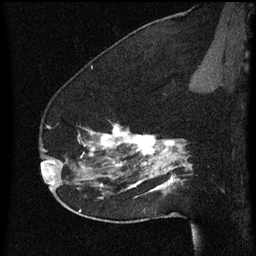
Breast MRI (dynamic contrast-enhanced), one sagittal slice. Dynamic contrast-enhanced series, image 2 of 3 at this slice position (ordered by acquisition). 1.5 T. TE 4.2 ms, TR 8 ms. 2 mm slice thickness. 256 × 256 image matrix. Female patient, age 52 years.
Outlined on this slice (semi-automatically segmented with operator editing):
- analysis volume of interest (the breast-tissue region the enhancement analysis was run in; not a lesion): box from (x=54, y=122) to (x=178, y=207) px
- tumour enhancement mask (voxels above the 70 % enhancement threshold inside the analysis volume of interest): (x=62, y=124)–(x=178, y=193)